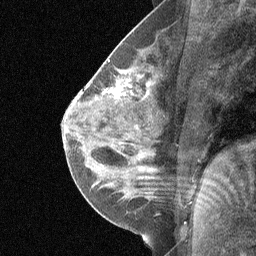
Breast MRI (dynamic contrast-enhanced), one sagittal slice; position 32 of 64 along the scan axis; dynamic contrast-enhanced study with each time point stored as its own series, time point 3 of 5 at this slice position (ordered by acquisition time); 1.5 T; TE 4.8 ms, TR 27 ms; 2 mm slice thickness; 256 × 256 image matrix. Female patient, age 26 years. Case-level facts recorded for this patient, not image findings: setting: breast cancer imaged before/during neoadjuvant chemotherapy; receptor status: HR-positive, HER2-negative.
Annotated regions visible in this slice (semi-automatic segmentation, software-assisted and operator-edited):
- analysis volume of interest (the breast-tissue region the enhancement analysis was run in; not a lesion): bounding box [x1, y1, x2, y2] px = [85, 46, 163, 144]
- tumour enhancement mask (voxels above the 90 % enhancement threshold inside the analysis volume of interest): [111, 86, 120, 95]